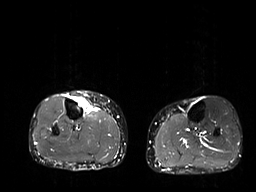
MRI of an extremity soft-tissue mass, one axial slice. Position 13 of 32 along the scan axis. STIR. 6 mm slice thickness. 256 × 192 image matrix. Female patient. From the clinical record (not read from this slice): histological type: undifferentiated – high grade; grade: high; site of the primary tumour: right thigh.
Outlined on this slice (manually delineated by an expert):
- gross tumour volume (mass): bounding box [x1, y1, x2, y2] px = [72, 95, 91, 114]